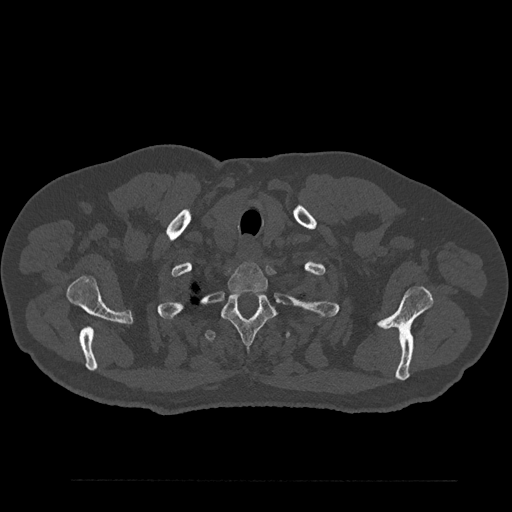
CT including the spine, one axial slice; position 722 of 797 along the scan axis; 120 kVp; bone window (W 1800 / L 400 HU); 512 × 512 image matrix, field of view 430 × 430 mm. Patient: male, 61 years. From the clinical record (not read from this slice): primary cancer: prostate.
Outlined on this slice (semi-automatic segmentation, software-assisted and operator-edited):
- T1 vertebra: box from (x=227, y=262) to (x=268, y=292) px
- T2 vertebra: (x=222, y=292)–(x=276, y=344)
- T3 vertebra: (x=204, y=330)–(x=291, y=342)